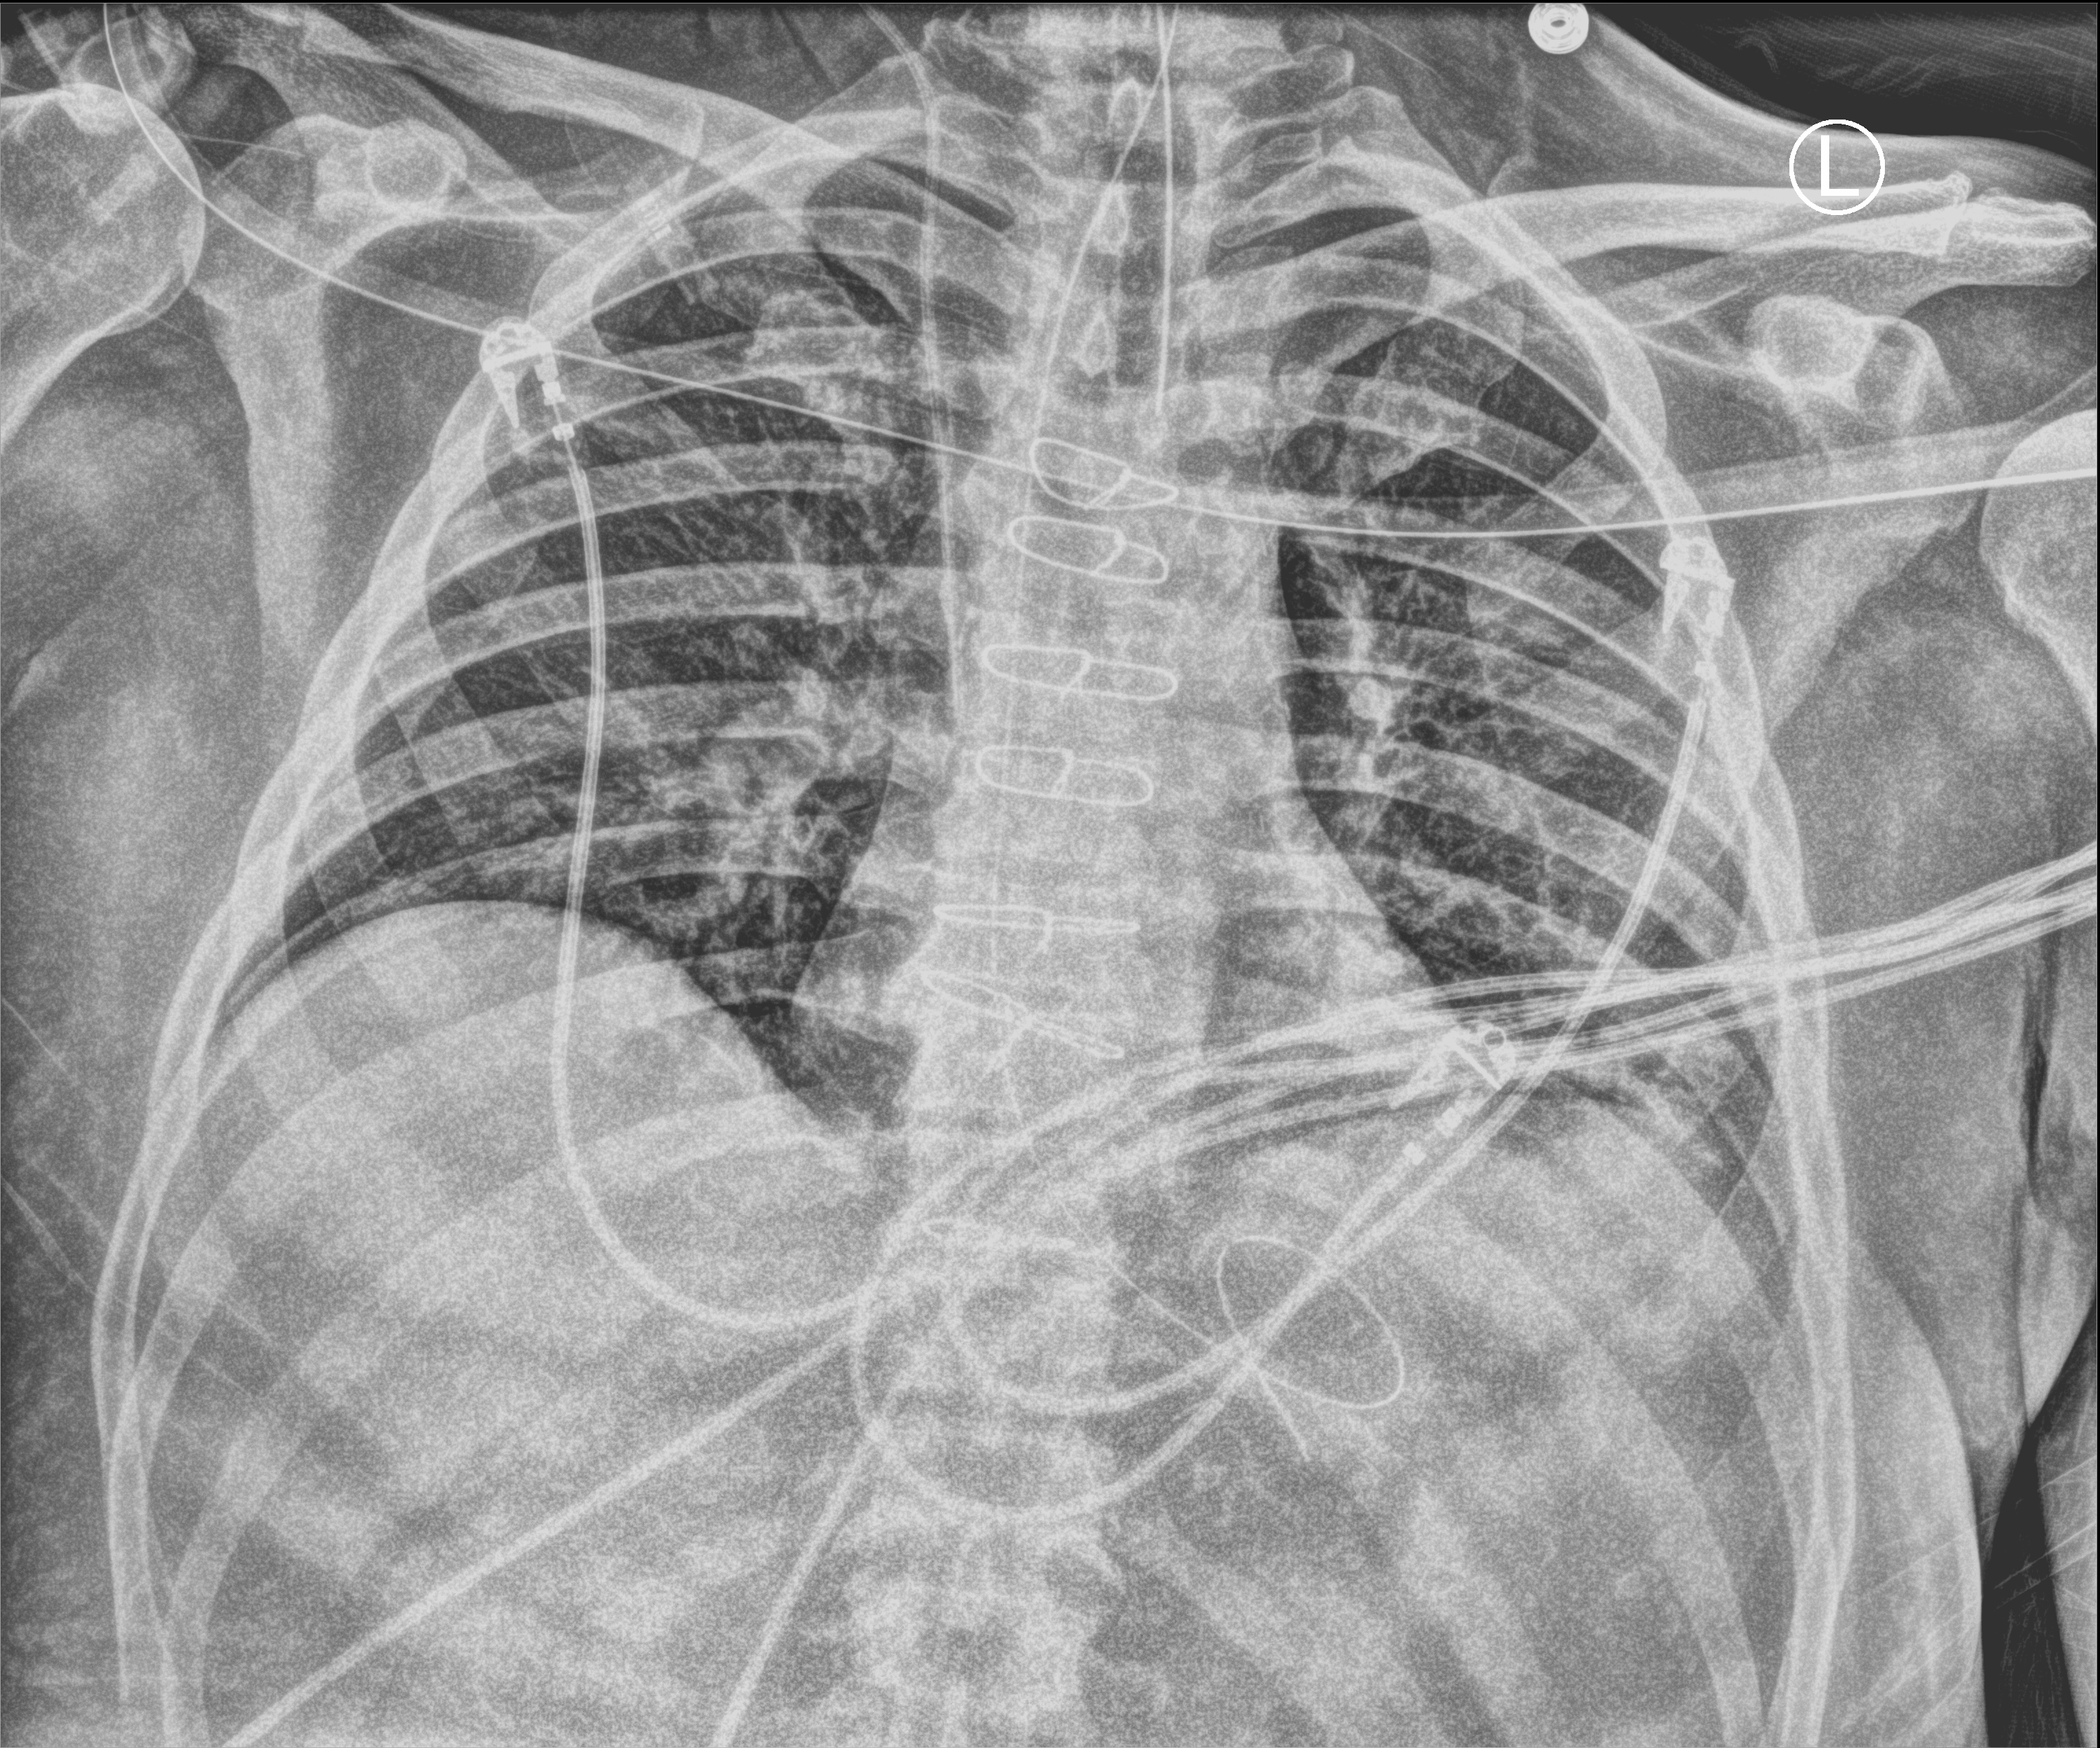
Portable chest radiograph. Patient hospitalised with COVID-19; male, aged 60–74 years.
From the hospital-stay record, not from the radiograph (when in the stay this image was taken is not recorded):
- COPD (admission record): no
- mechanically ventilated during this hospital stay: yes